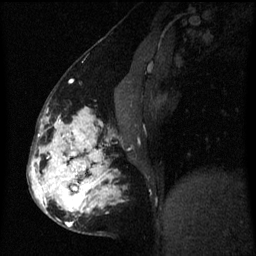
Breast MRI (dynamic contrast-enhanced), one sagittal slice. Position 27 of 60 along the scan axis. Dynamic contrast-enhanced series, image 2 of 3 at this slice position (ordered by acquisition). 1.5 T. TE 4.2 ms, TR 8 ms. 2 mm slice thickness. 256 × 256 image matrix, field of view 190 × 190 mm. Patient: female, 50 years.
Annotated regions visible in this slice (semi-automatically segmented with operator editing):
- analysis volume of interest (the breast-tissue region the enhancement analysis was run in; not a lesion): bounding box [x1, y1, x2, y2] px = [32, 107, 114, 233]
- tumour enhancement mask (voxels above the 70 % enhancement threshold inside the analysis volume of interest): [32, 107, 112, 227]